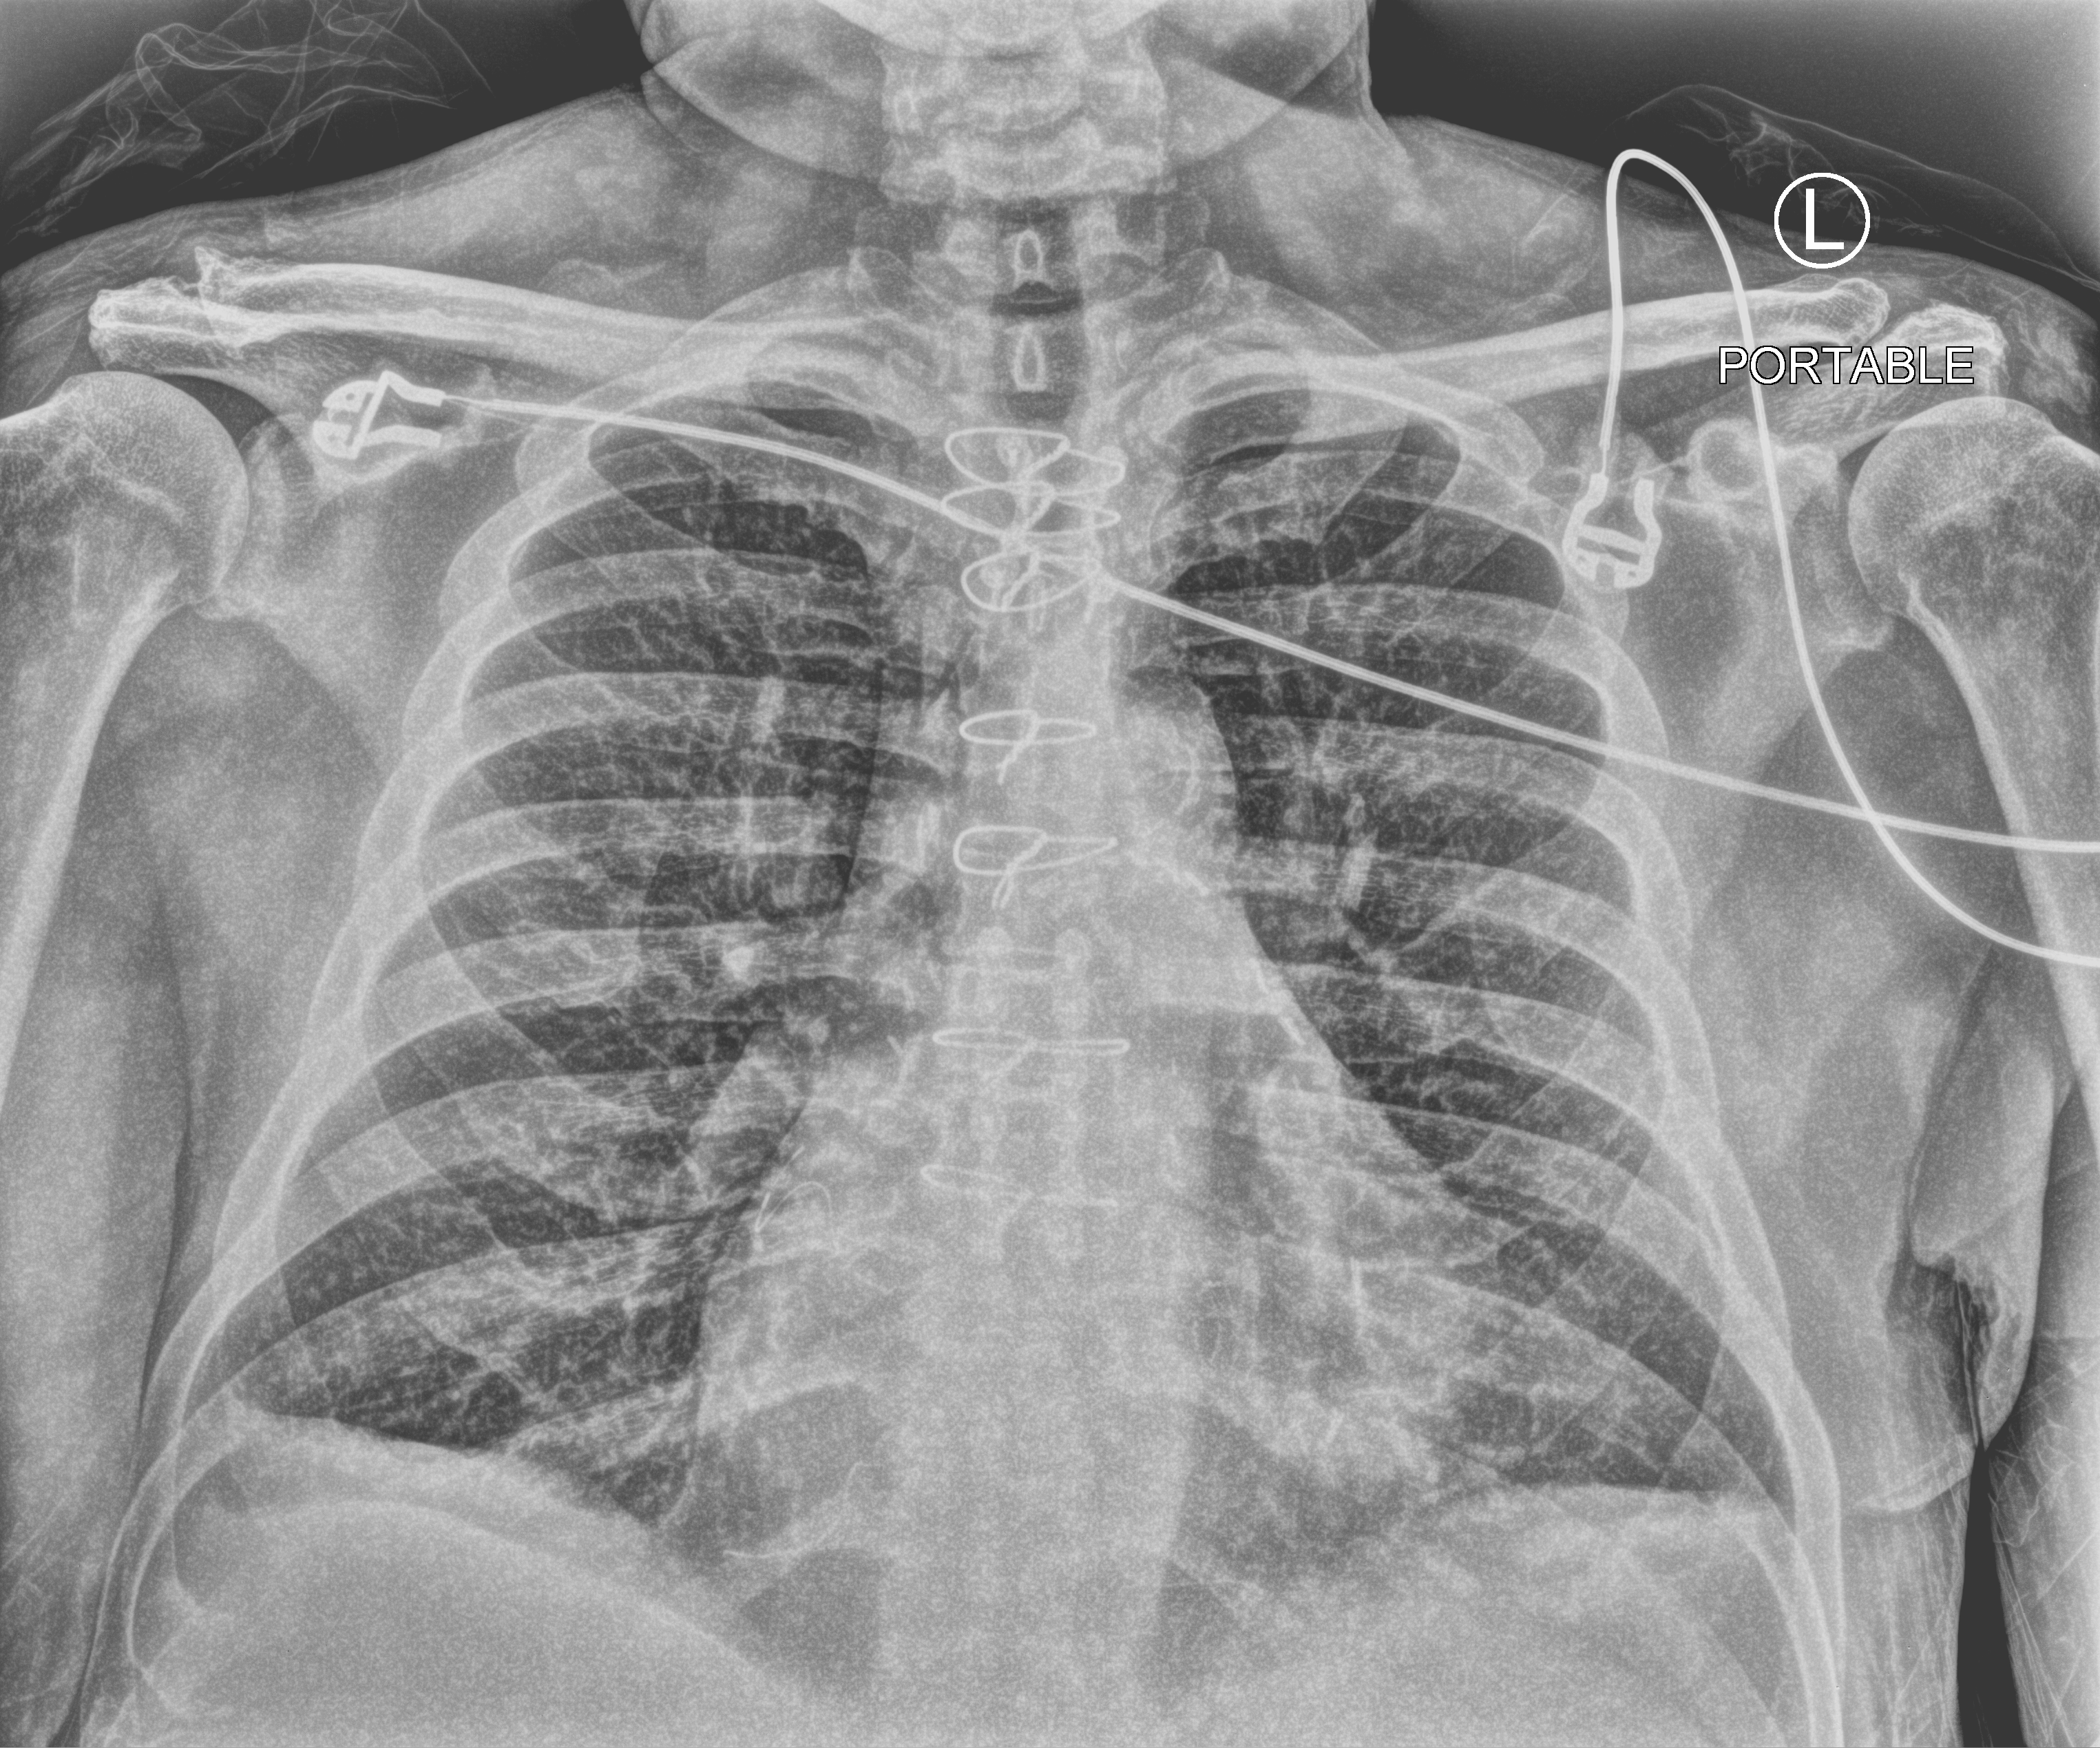
Portable chest radiograph, anteroposterior (AP) projection. Male patient hospitalised with COVID-19, age 60–74 years.
Admission-level facts for this patient (not findings on this image; timing relative to this image not recorded): chronic kidney disease (admission record): no; mechanically ventilated during this hospital stay: no.